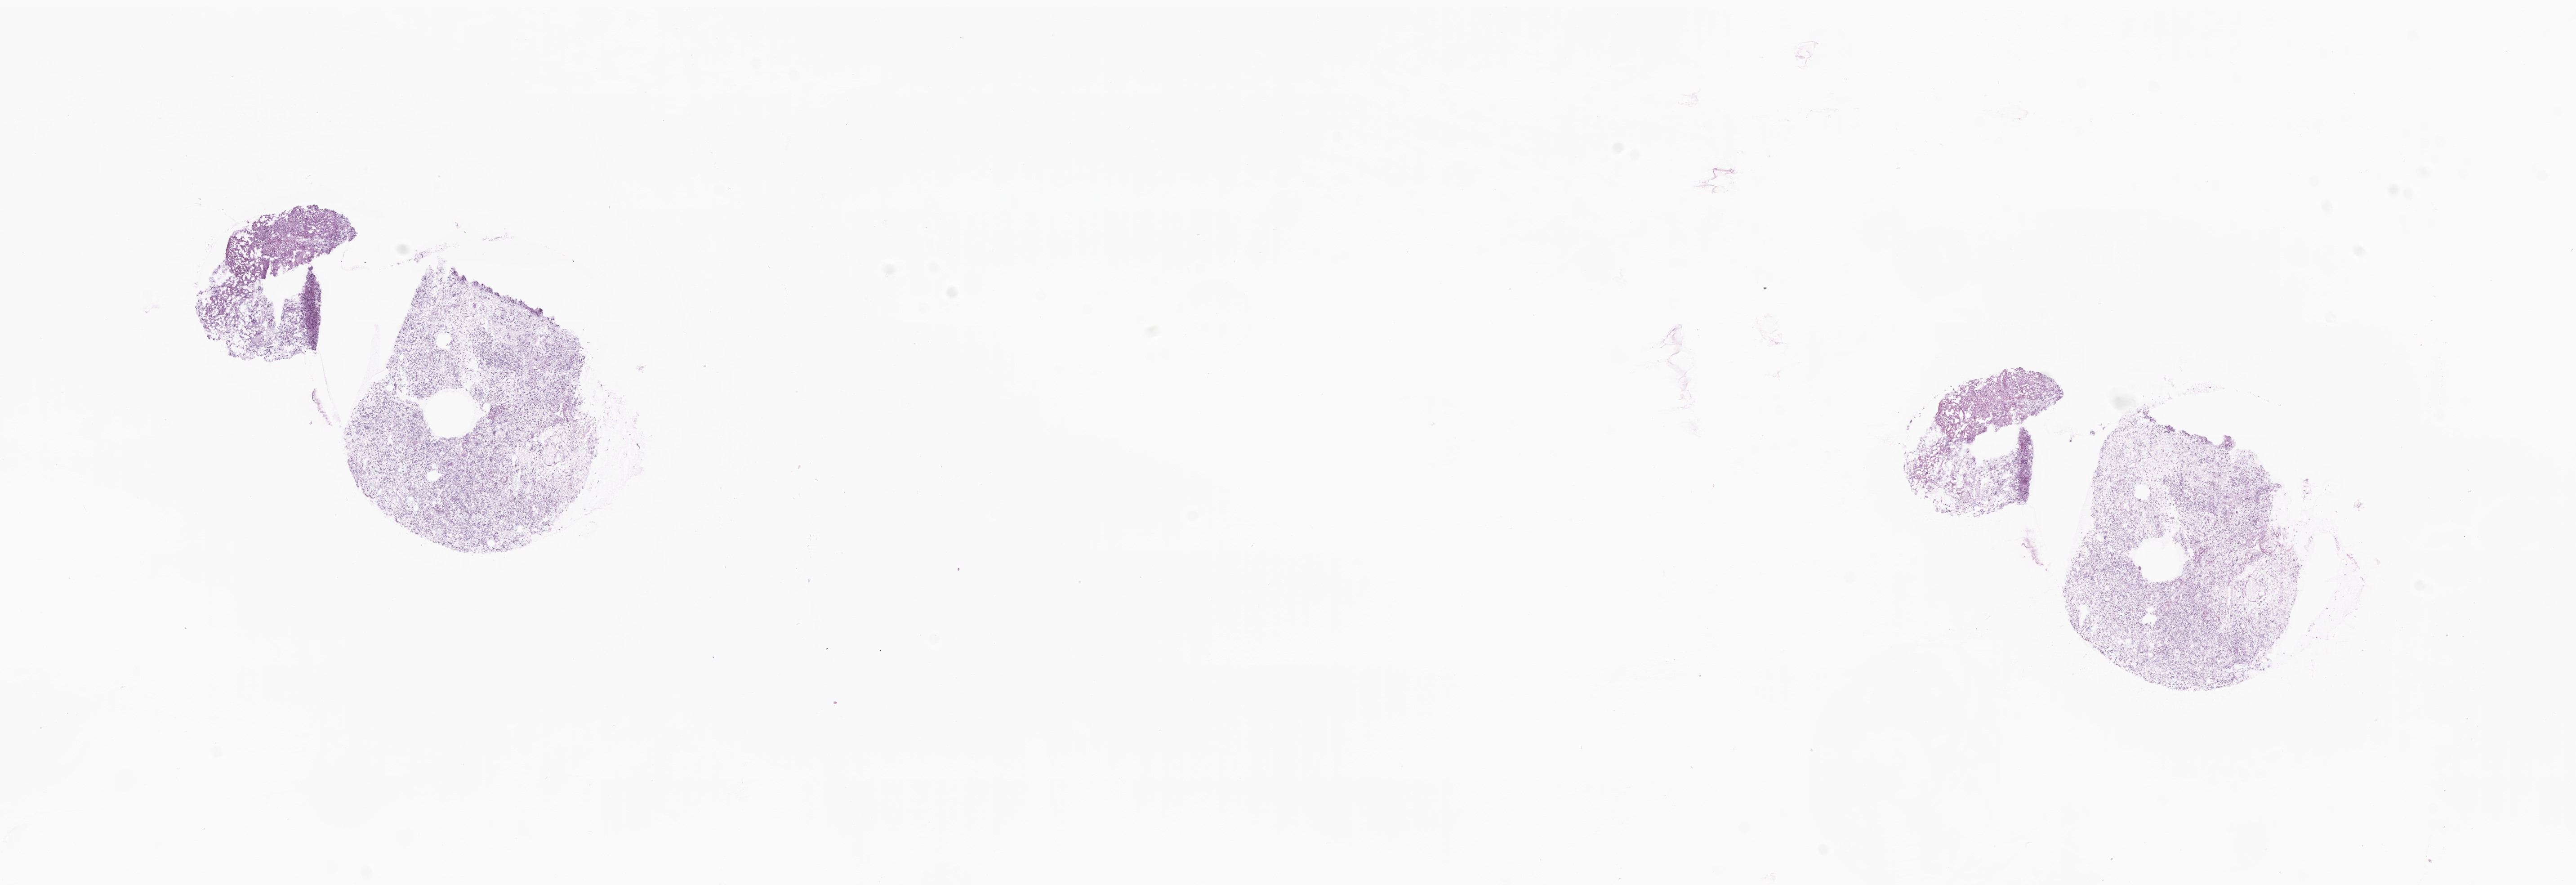
H&E whole-slide image, whole scanned area (about 24.2 x 8.3 mm) shown as a low-resolution overview, cryosection, recurrent tumor, anatomic site: brain. Patient: female, age at initial diagnosis 58 years. Composition of this section per pathologist review: tumor cells 98%, tumor nuclei 98%, stromal cells 0%, necrosis 2%, normal cells 0%. Infiltration values recorded for this section: lymphocyte infiltration 0%, monocyte infiltration 0%, neutrophil infiltration 0%.
• section: top of the tissue portion
• patient diagnosis: Glioblastoma, NOS